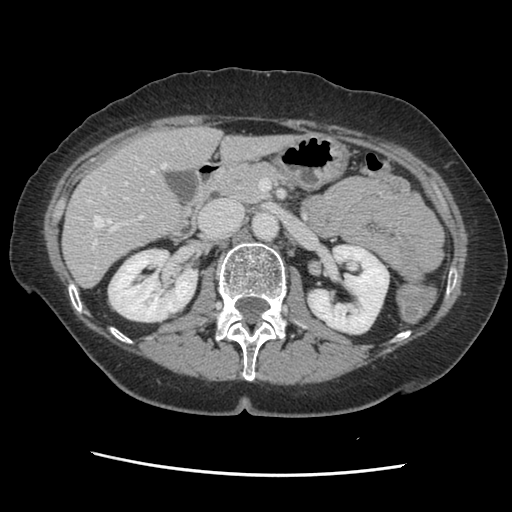
Contrast-enhanced abdominal CT, one axial slice. Position 70 of 141 along the scan axis. 120 kVp. Soft-tissue window (W 400 / L 40 HU). 512 × 512 image matrix, field of view 330 × 330 mm. Female patient, age 61 years. Case-level facts recorded for this patient, not image findings: diagnosis: colorectal cancer liver metastases, imaged before liver resection; multiple liver metastases: no; largest metastasis: 2.4 cm; chemotherapy before resection: no.
Structures marked on this image (outlined manually by an expert reader):
- hepatic veins: bounding box <89,163,166,228> (left, top, right, bottom; pixels)
- liver: <63,127,291,286>
- planned liver remnant (the part of the liver to remain after resection): <63,127,292,286>
- portal vein (with intrahepatic branches): <92,182,144,249>